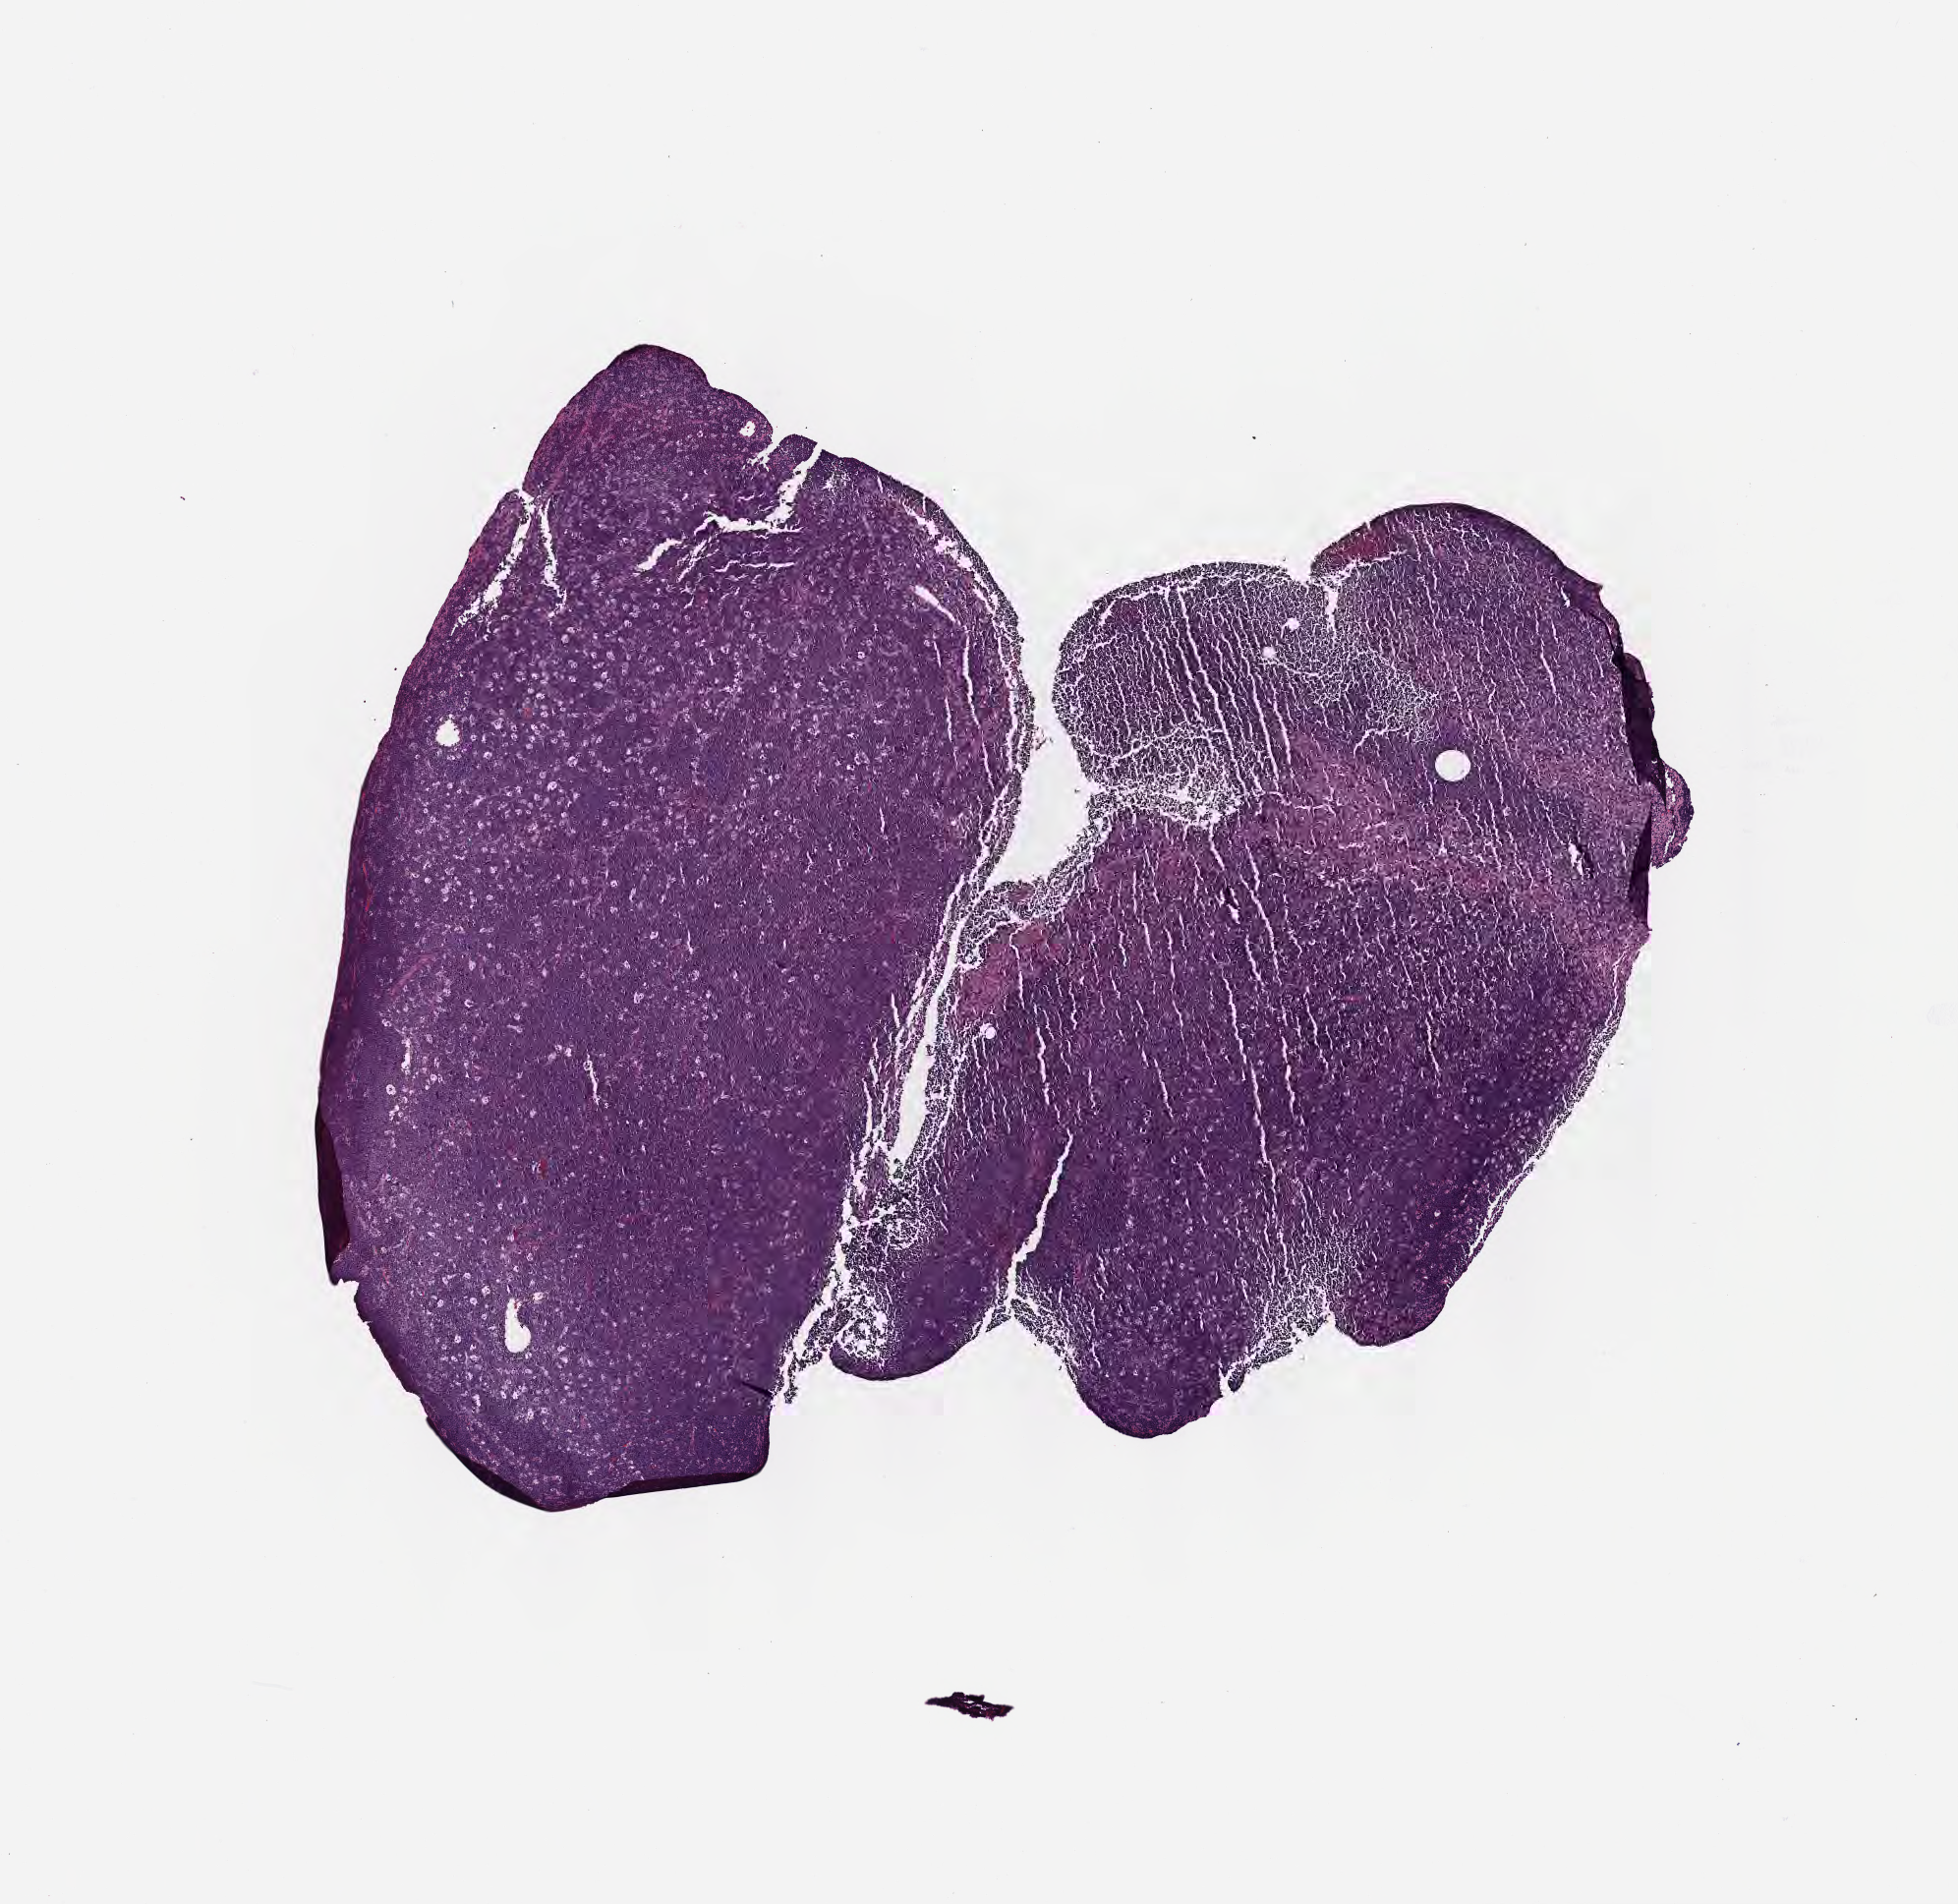
Digitized haematoxylin and eosin-stained section — whole scanned area (about 8.0 x 7.8 mm) shown as a low-resolution overview; FFPE section; specimen: primary tumor. Male patient, aged 45. Composition of this section per pathologist review: tumor cells 95%, tumor nuclei 95%, stromal cells 5%, necrosis 0%, normal cells 0%. Infiltration values recorded for this section: lymphocyte infiltration 15%, monocyte infiltration 40%, neutrophil infiltration 5%.
* diagnosis: Burkitt lymphoma, NOS
* Ann Arbor stage (patient): Stage IV